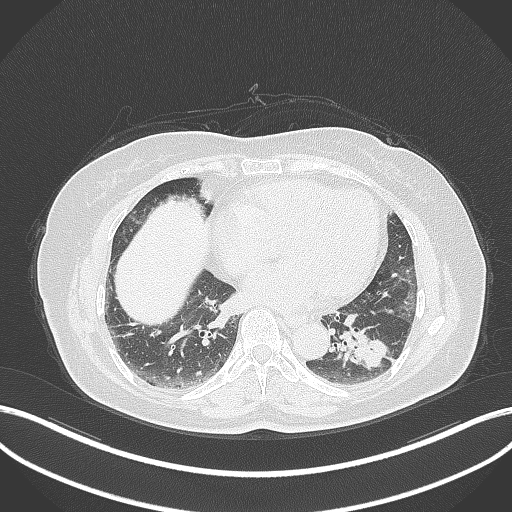
Chest CT, one axial slice. Slice 144 of 311 in the series (ordered by position). Reconstruction kernel B70f. 120 kVp. Lung window (W 1500 / L -600 HU). 1 mm slice thickness. 512 × 512 image matrix. Patient: female, 59 years. Case-level facts recorded for this patient, not image findings: clinical TNM (as recorded): T2a N0 M0; histopathological grade: G2-3.
Annotated regions visible in this slice (bounding box drawn by a radiologist):
- lung tumour (recorded histology: adenocarcinoma): box from (x=334, y=320) to (x=390, y=372) px